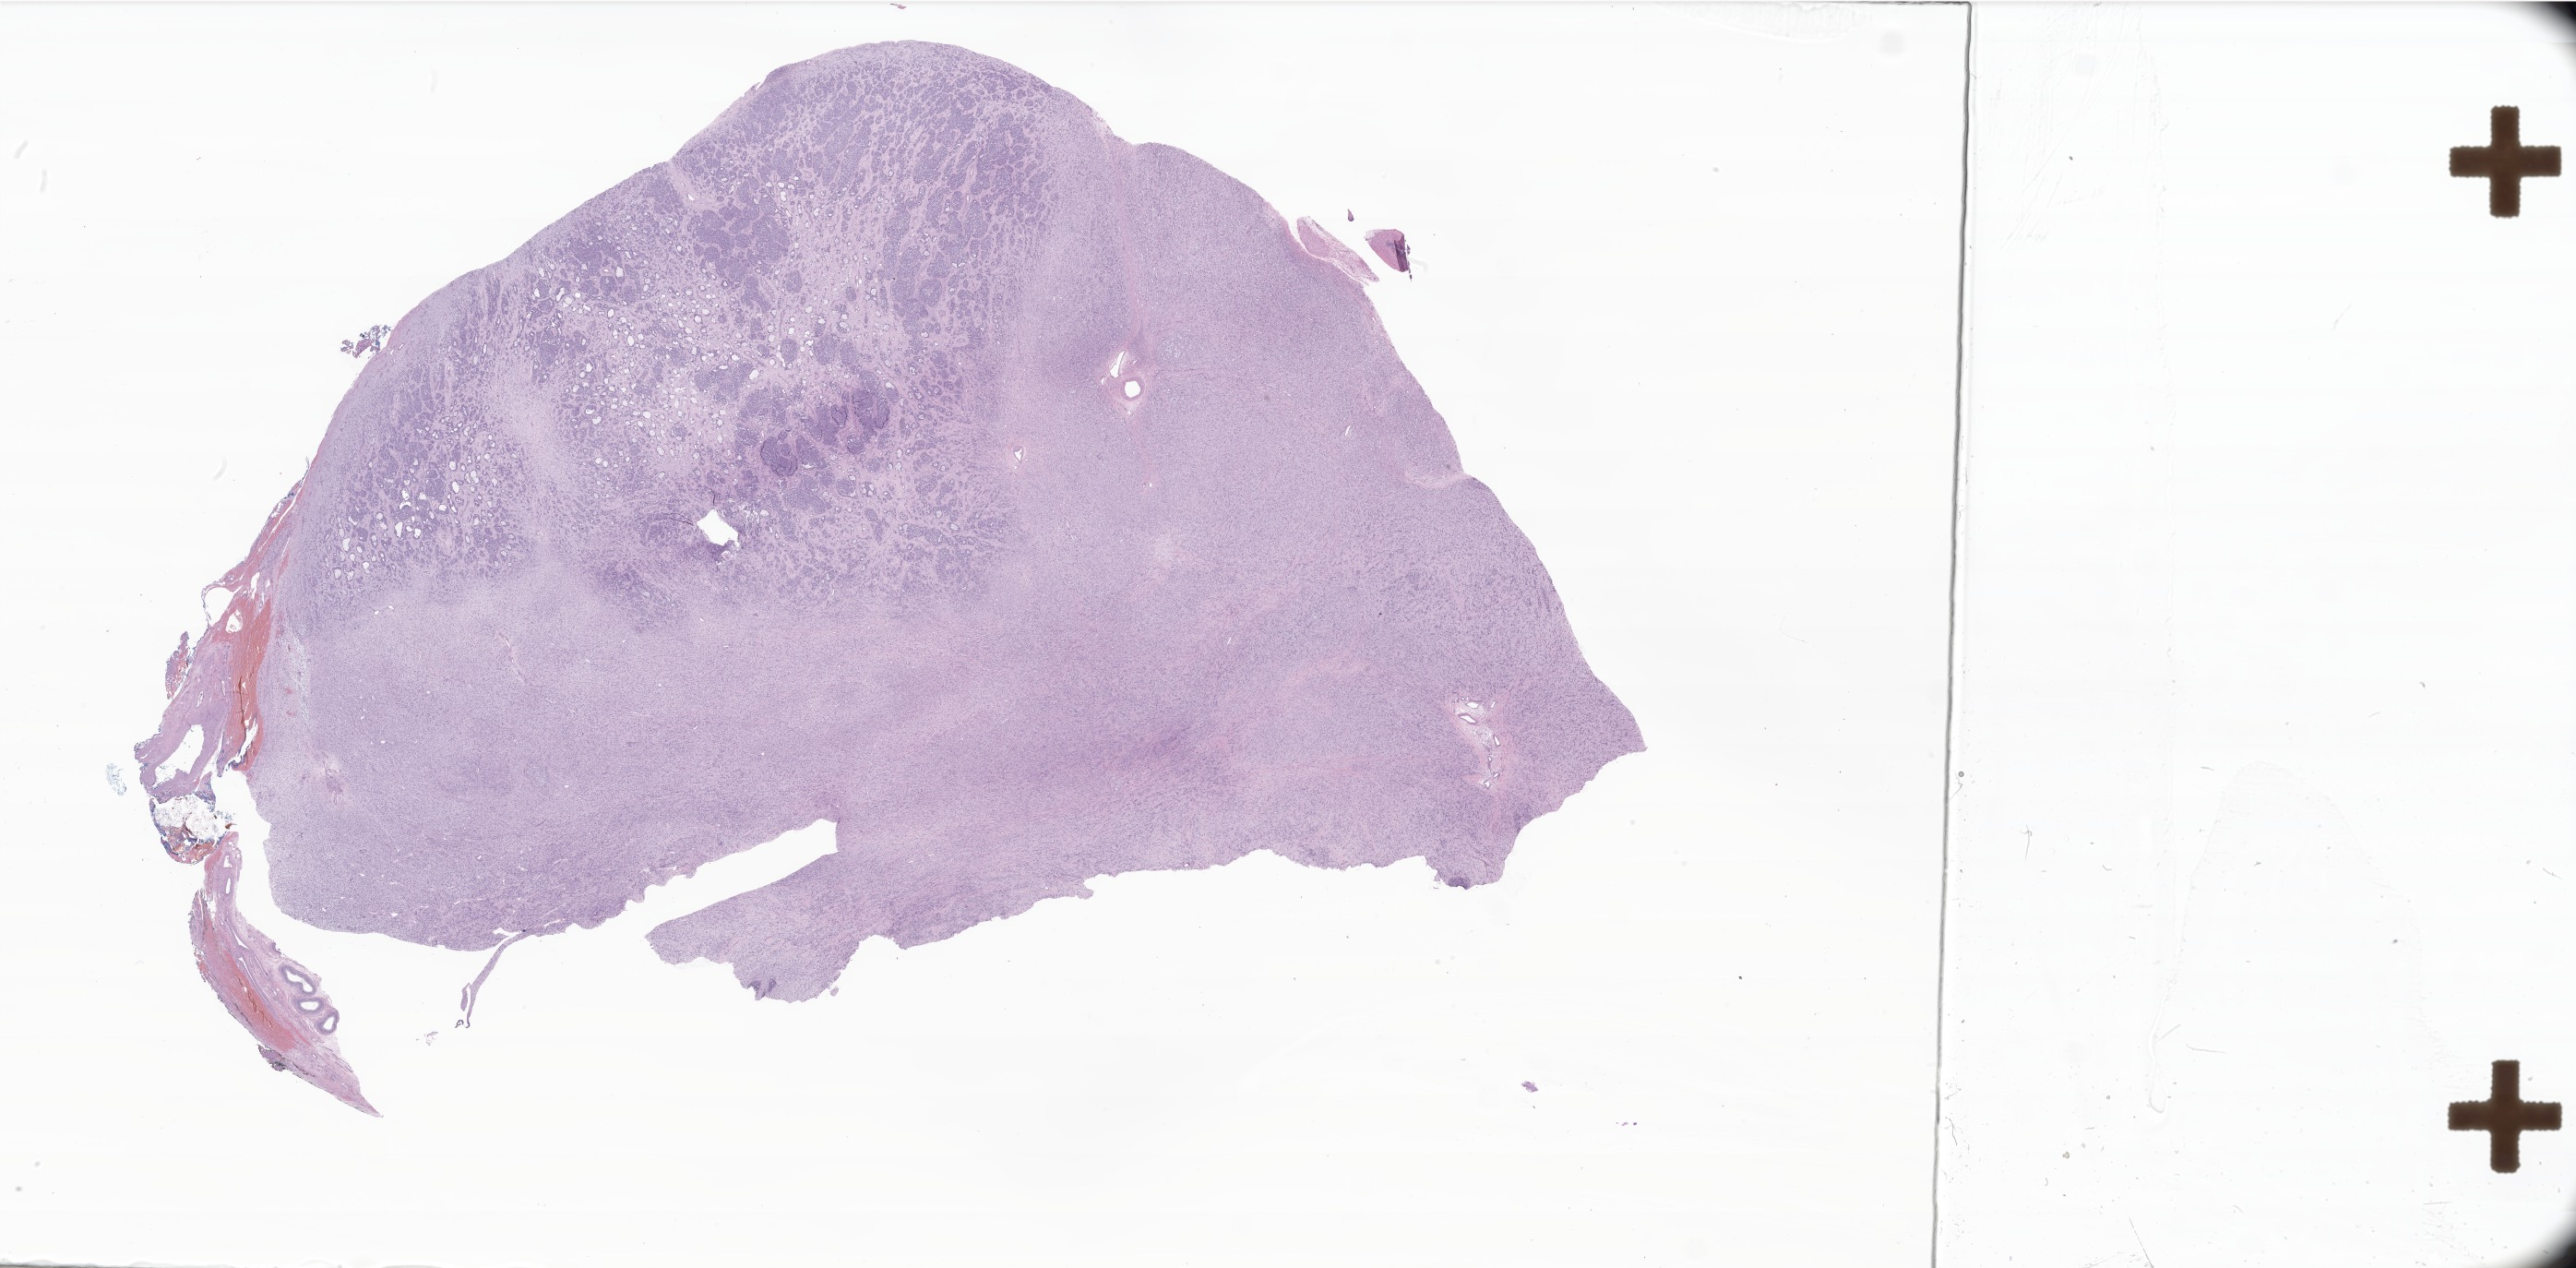
Digitized hematoxylin and eosin (H&E)-stained section of tumor tissue from the testis — a low-resolution overview of the entire scanned area, about 47.1 x 23.2 mm; formalin-fixed paraffin-embedded section. Patient male; age 183 months (15 years 3 months).
- recorded diagnosis: Embryonal rhabdomyosarcoma, NOS